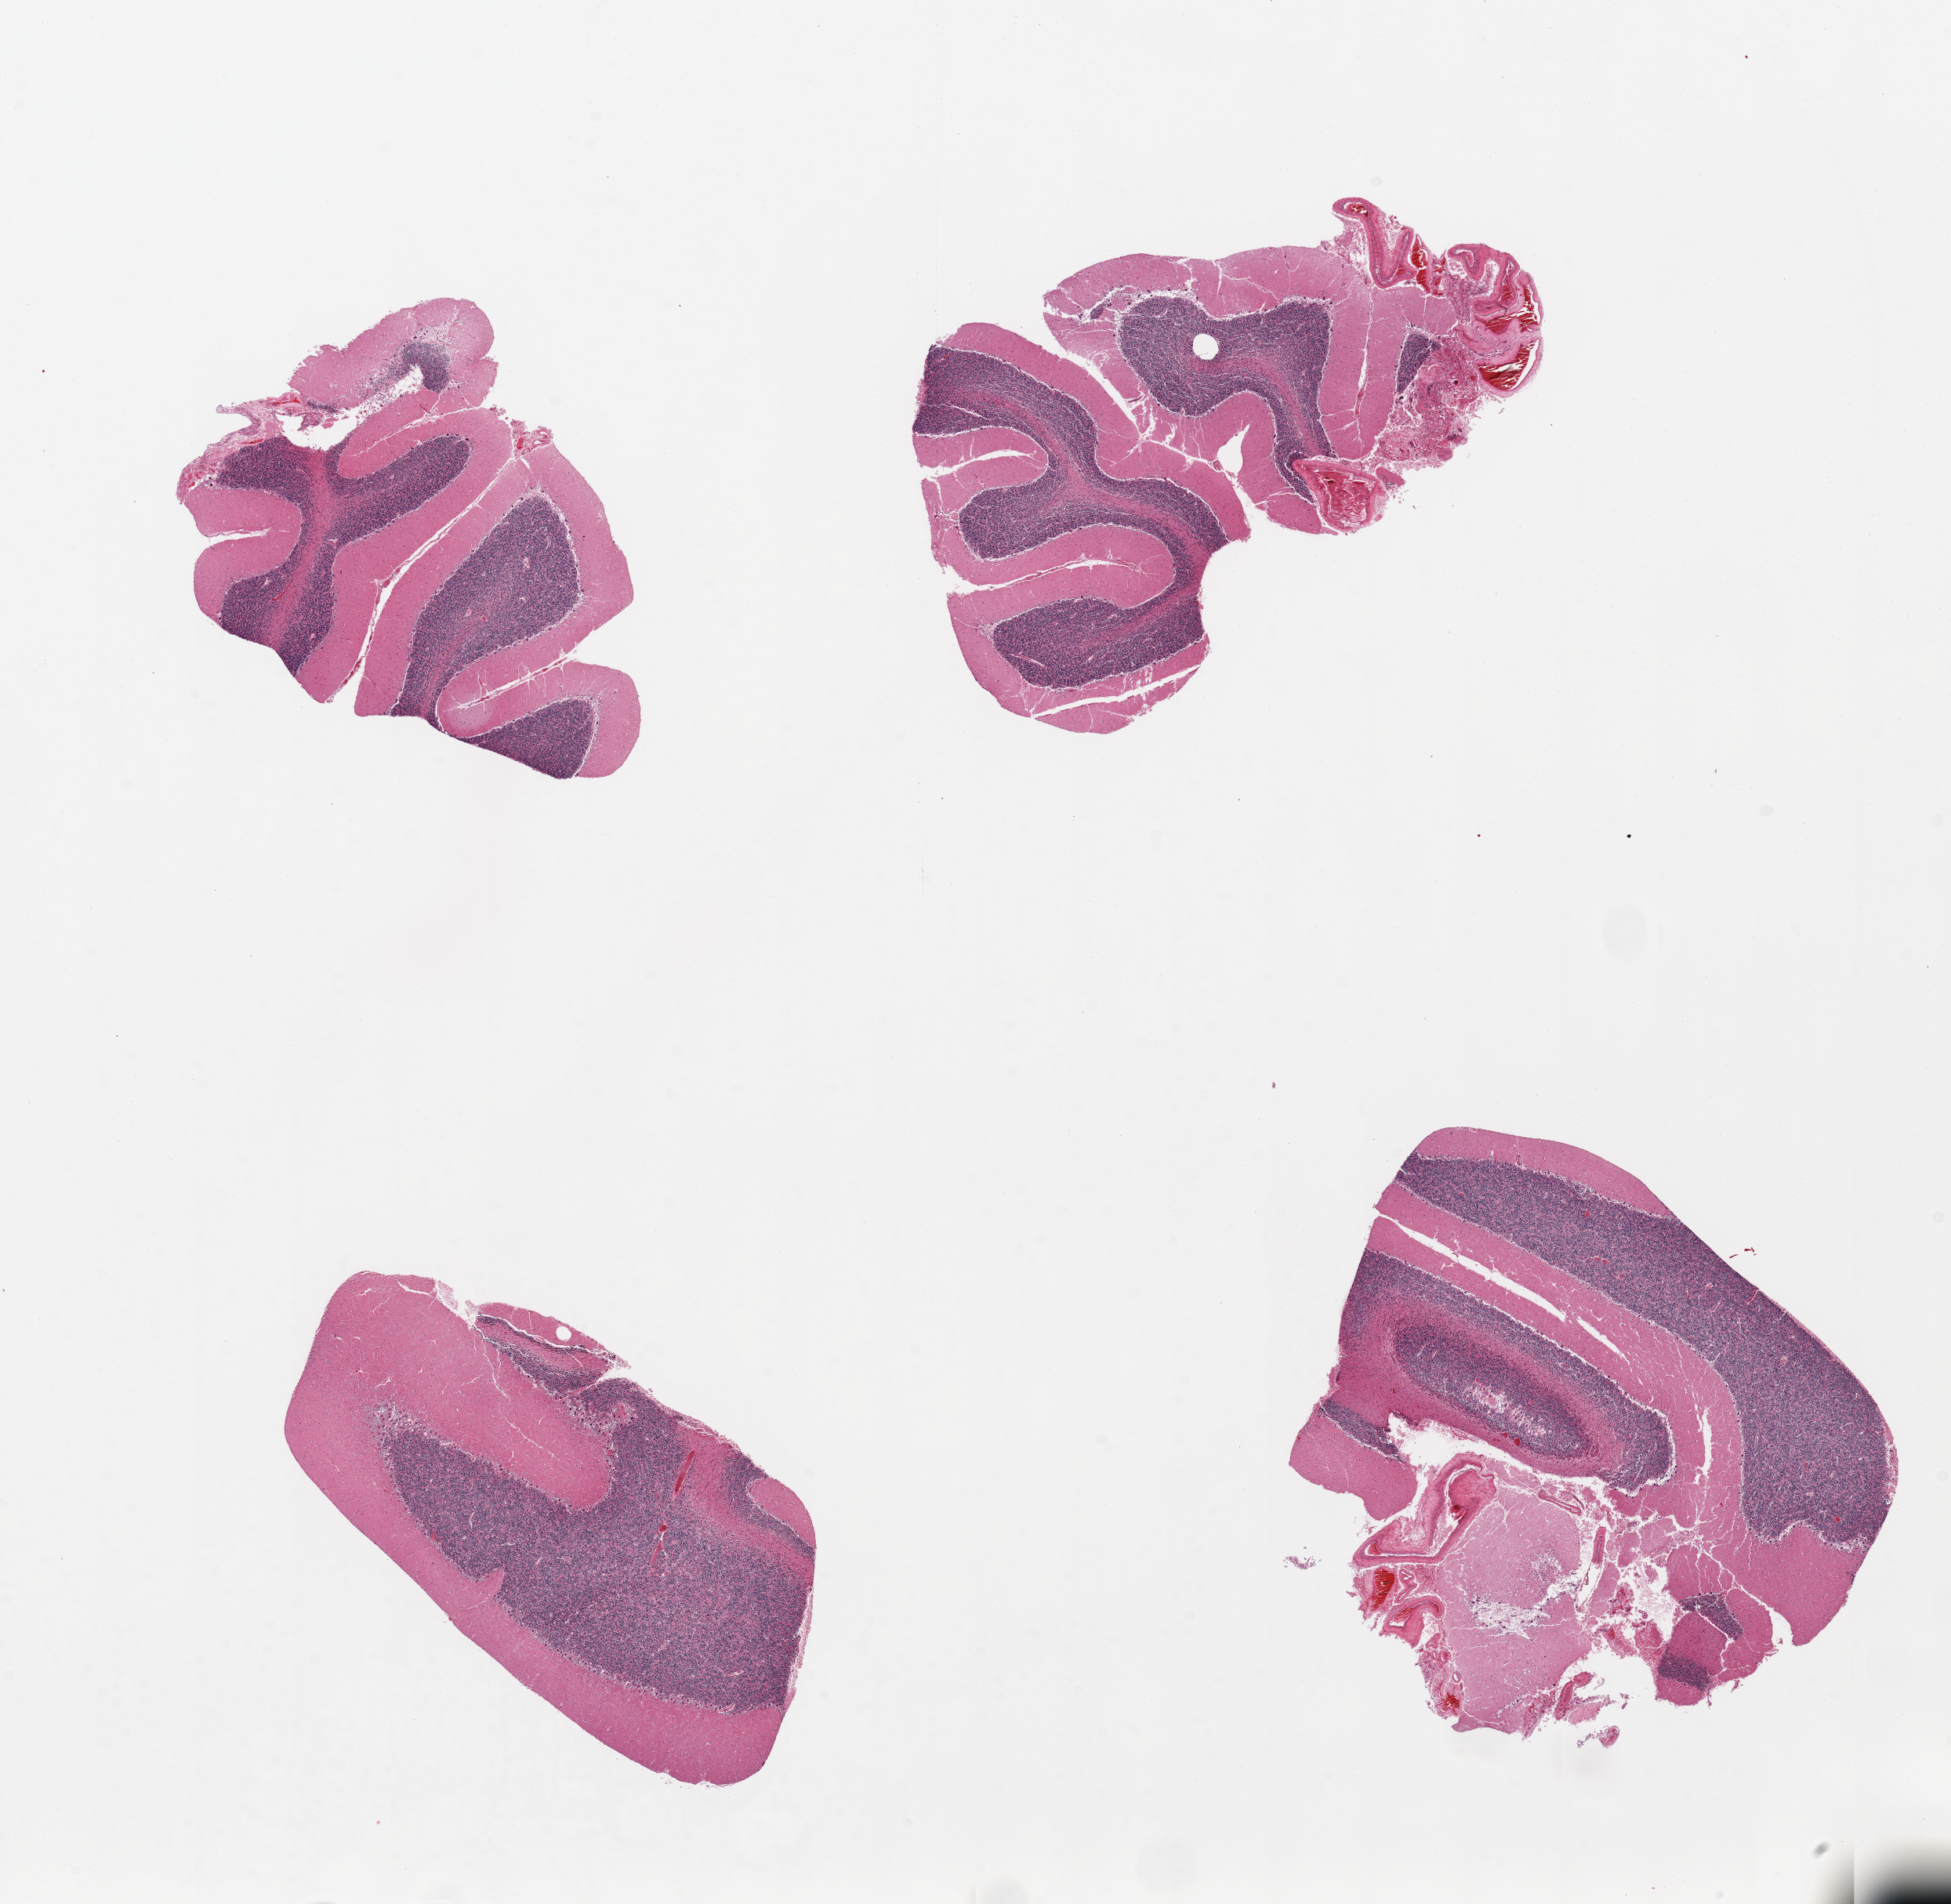
Haematoxylin and eosin whole-slide image, brightfield — shown as a low-resolution overview of the whole scanned area (about 19.7 x 19.2 mm, slide scanned at 20x), PAXgene-fixed paraffin-embedded (PFPE) section, target tissue: cerebellum, tissue donor sample. Donor sex: female.
Reviewer comment on this tissue sample: 4 pieces, moderately autolyzed.